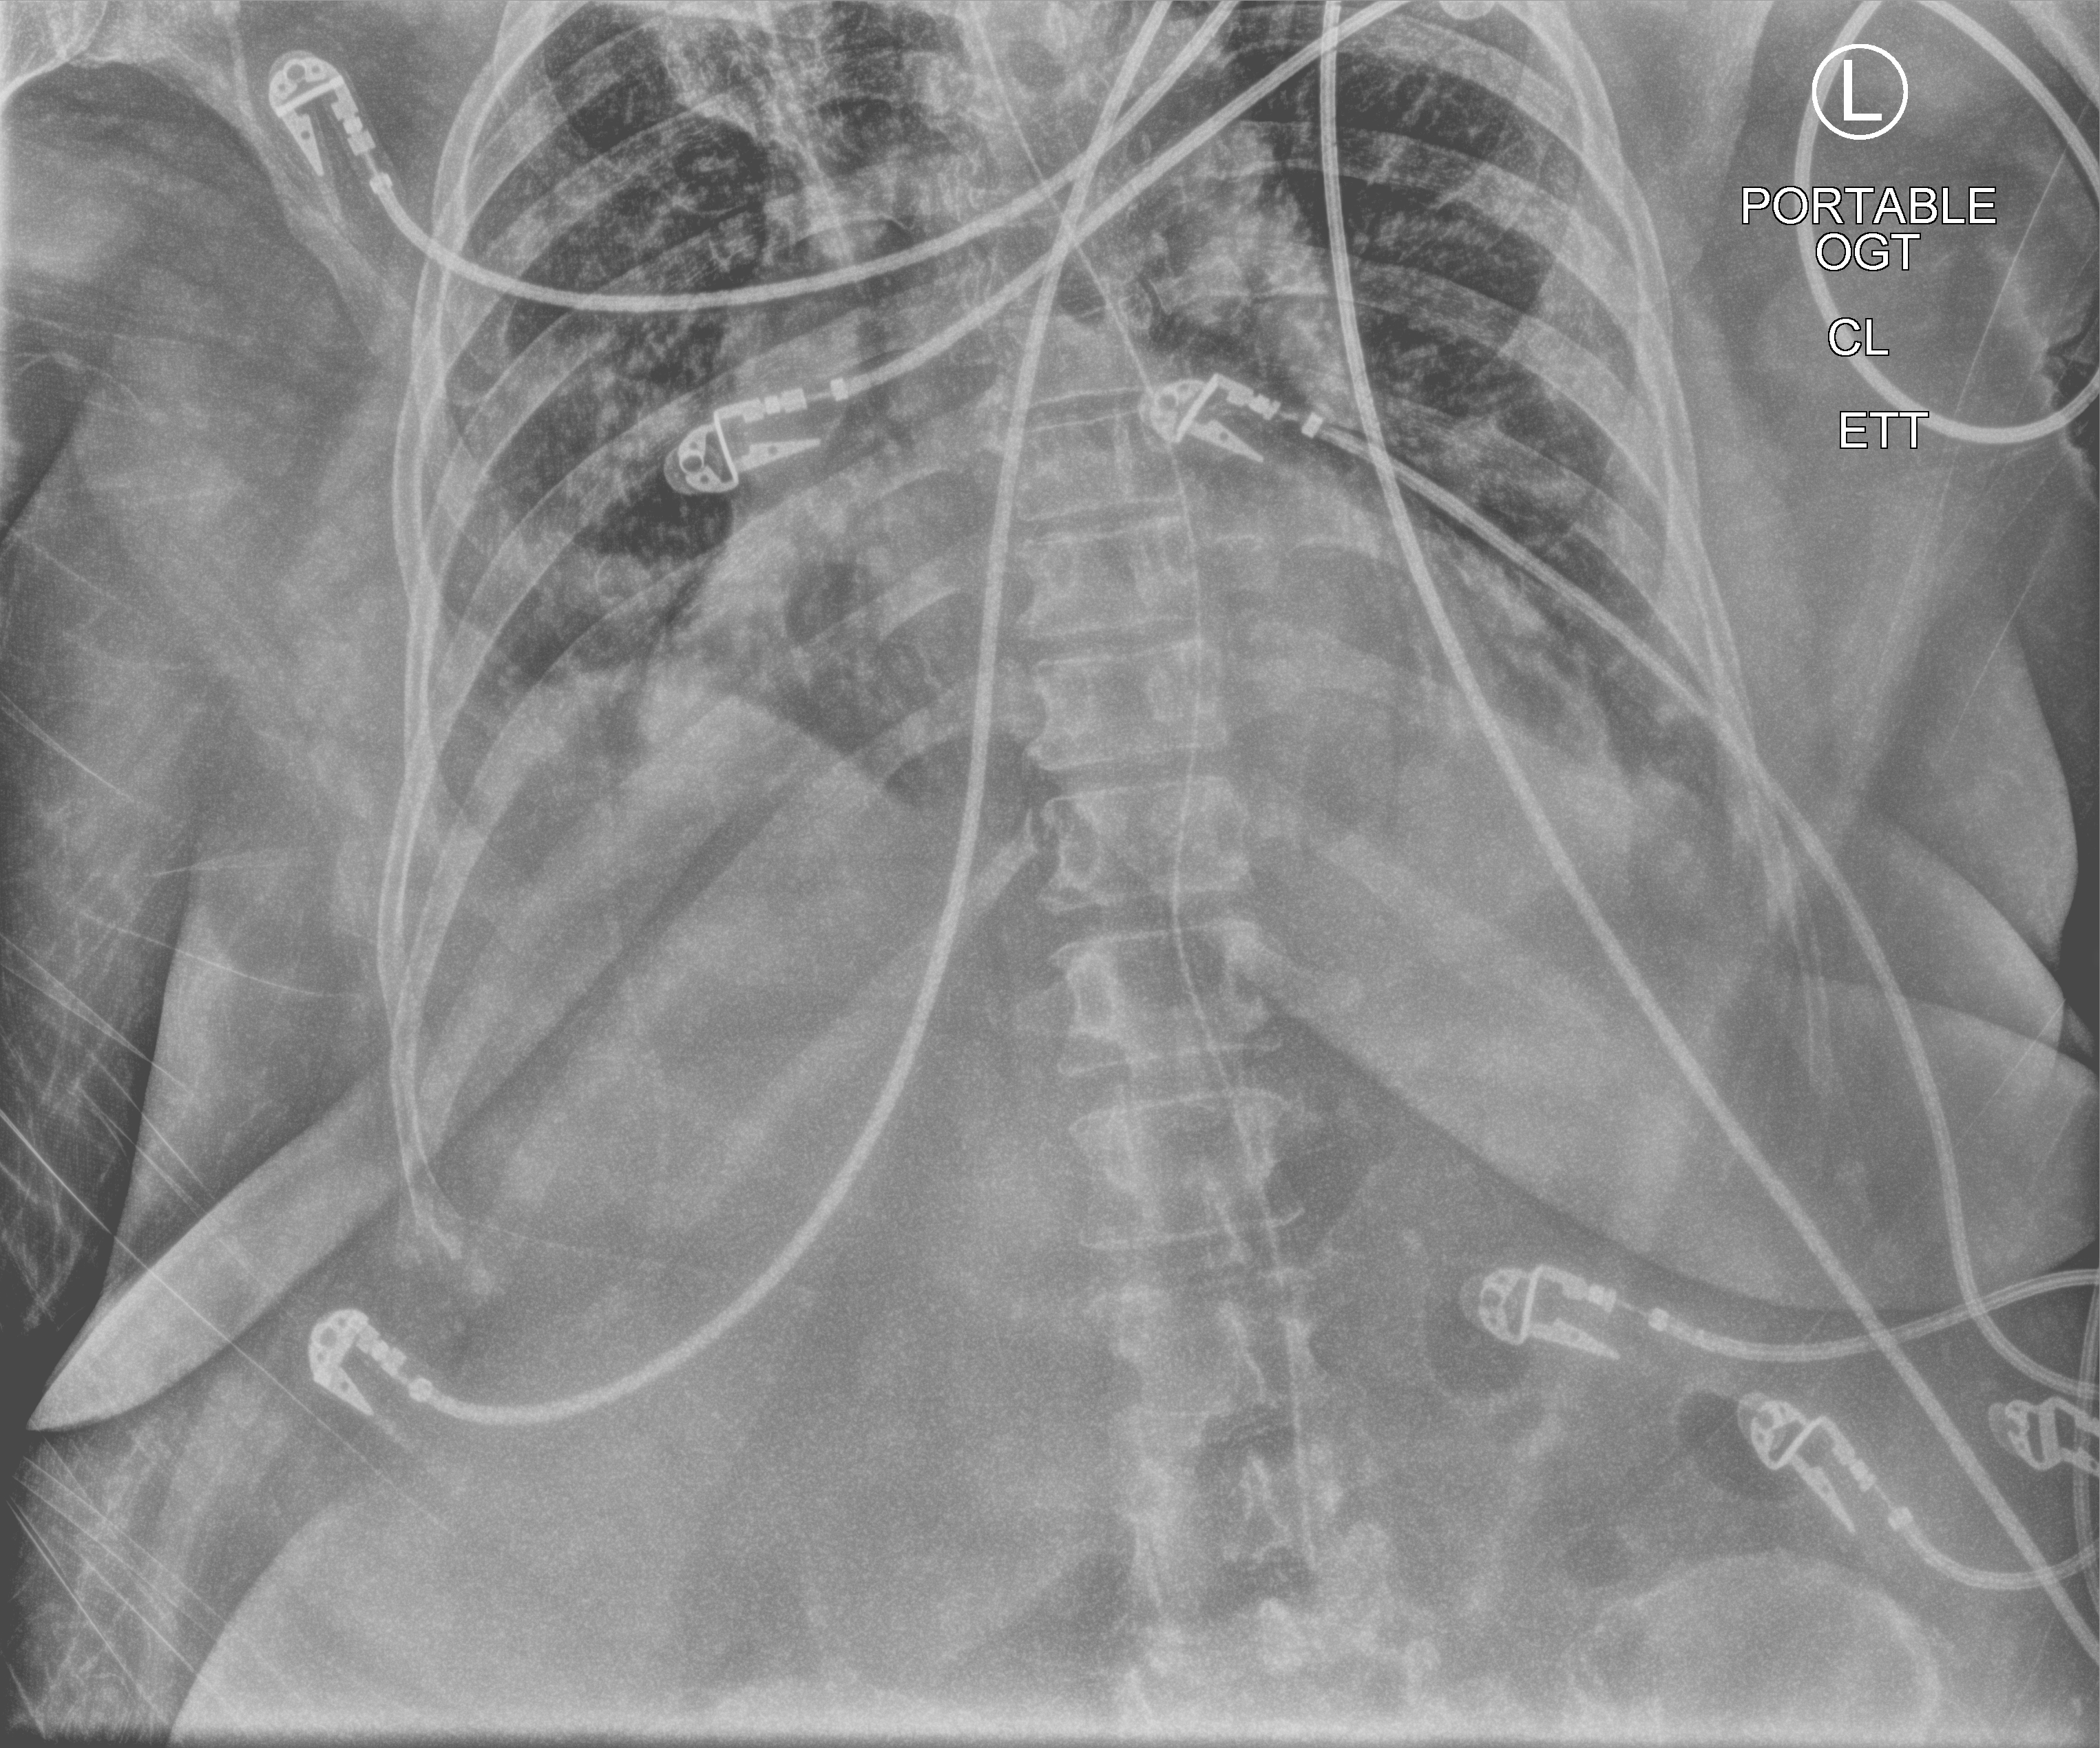
Chest X-ray (portable), anteroposterior (AP) projection. Patient hospitalised with COVID-19; female, aged 60–74 years.
Admission-level facts for this patient (not findings on this image; timing relative to this image not recorded):
- mechanically ventilated during this hospital stay: yes
- smoking status (admission record): never
- length of hospital stay: 9 days